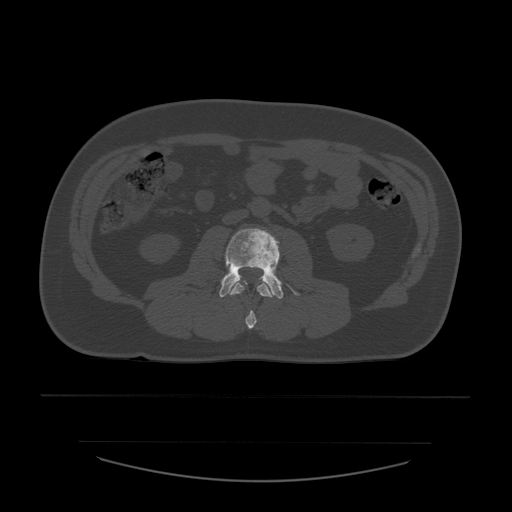
CT including the spine, one axial slice. Position 182 of 532 along the scan axis. Bone window (W 1800 / L 400 HU). 1.25 mm slice thickness. 512 × 512 image matrix, field of view 441 × 441 mm. Patient age 44 years. From the clinical record (not read from this slice): primary cancer: soft tissue sarcoma.
Annotated regions visible in this slice (semi-automatic segmentation, software-assisted and operator-edited):
- L2 vertebra: bounding box <231,282,274,329> (left, top, right, bottom; pixels)
- L3 vertebra: <220,228,299,299>